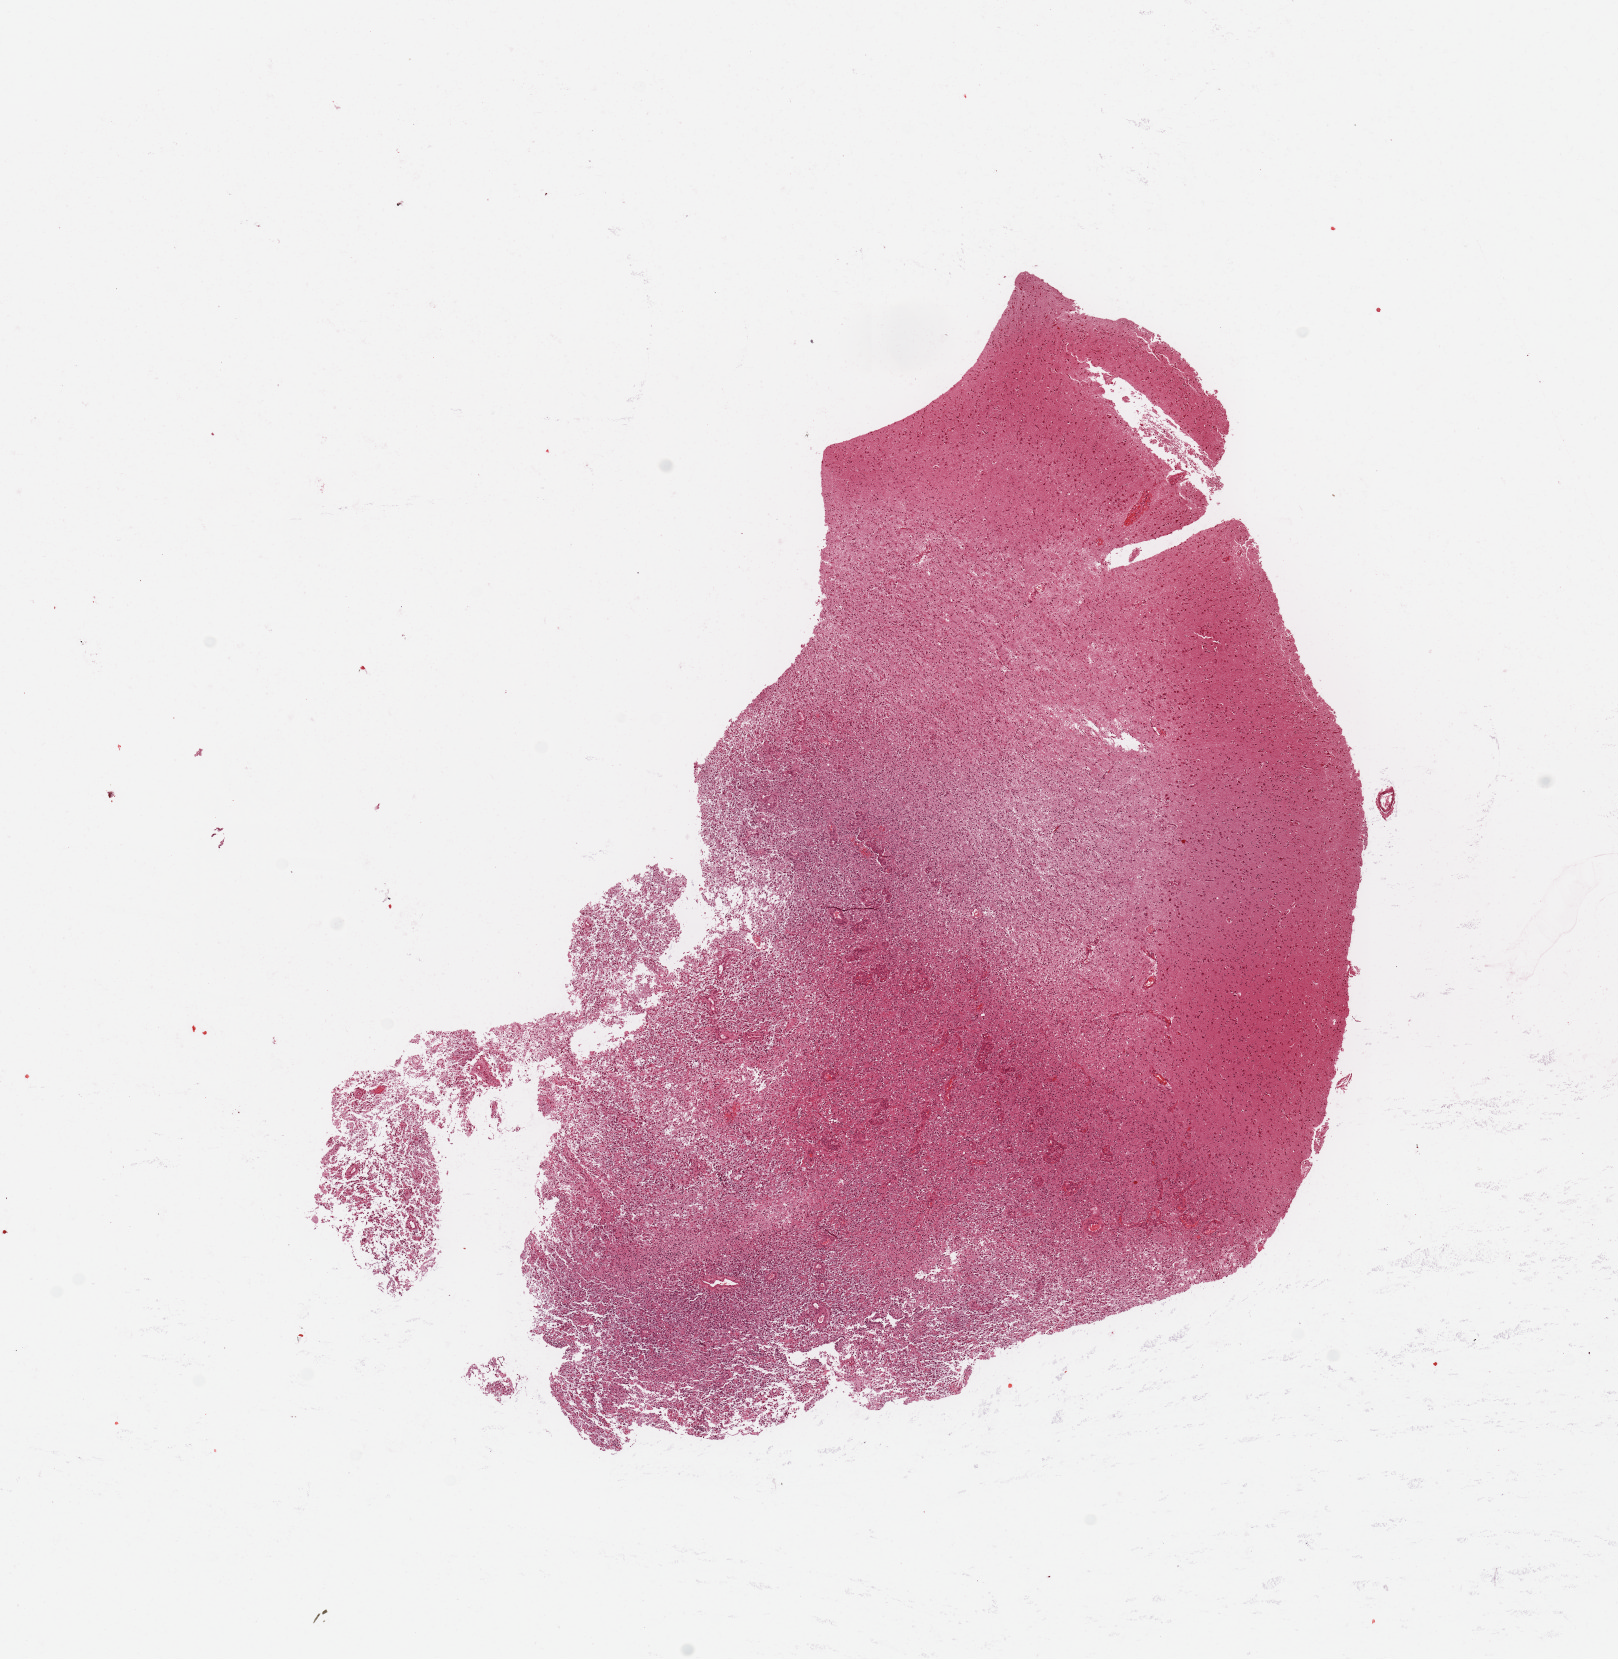
Whole-slide histology image, H&E-stained — a low-resolution overview of the entire scanned area, about 12.8 x 13.1 mm (slide scanned at 20x); tumour tissue sample, brain. 62-year-old female patient.
Primary tumour site (as recorded): parietal lobe. Patient diagnosis (cohort enrolment): glioblastoma multiforme (brain).